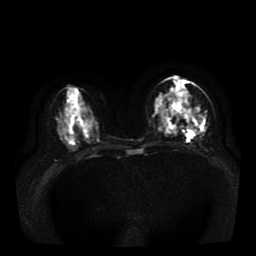
Breast MRI, one axial slice. Slice 17 of 41 in the series (ordered by position). Diffusion-weighted series; image 2 of 4 stored at this slice position (different b-values; order by instance number). 1.5 T. 5 mm slice thickness. 256 × 256 image matrix. Female patient.
Outlined on this slice (manually delineated by an expert):
- tumour on diffusion-weighted imaging: box from (x=182, y=111) to (x=198, y=134) px